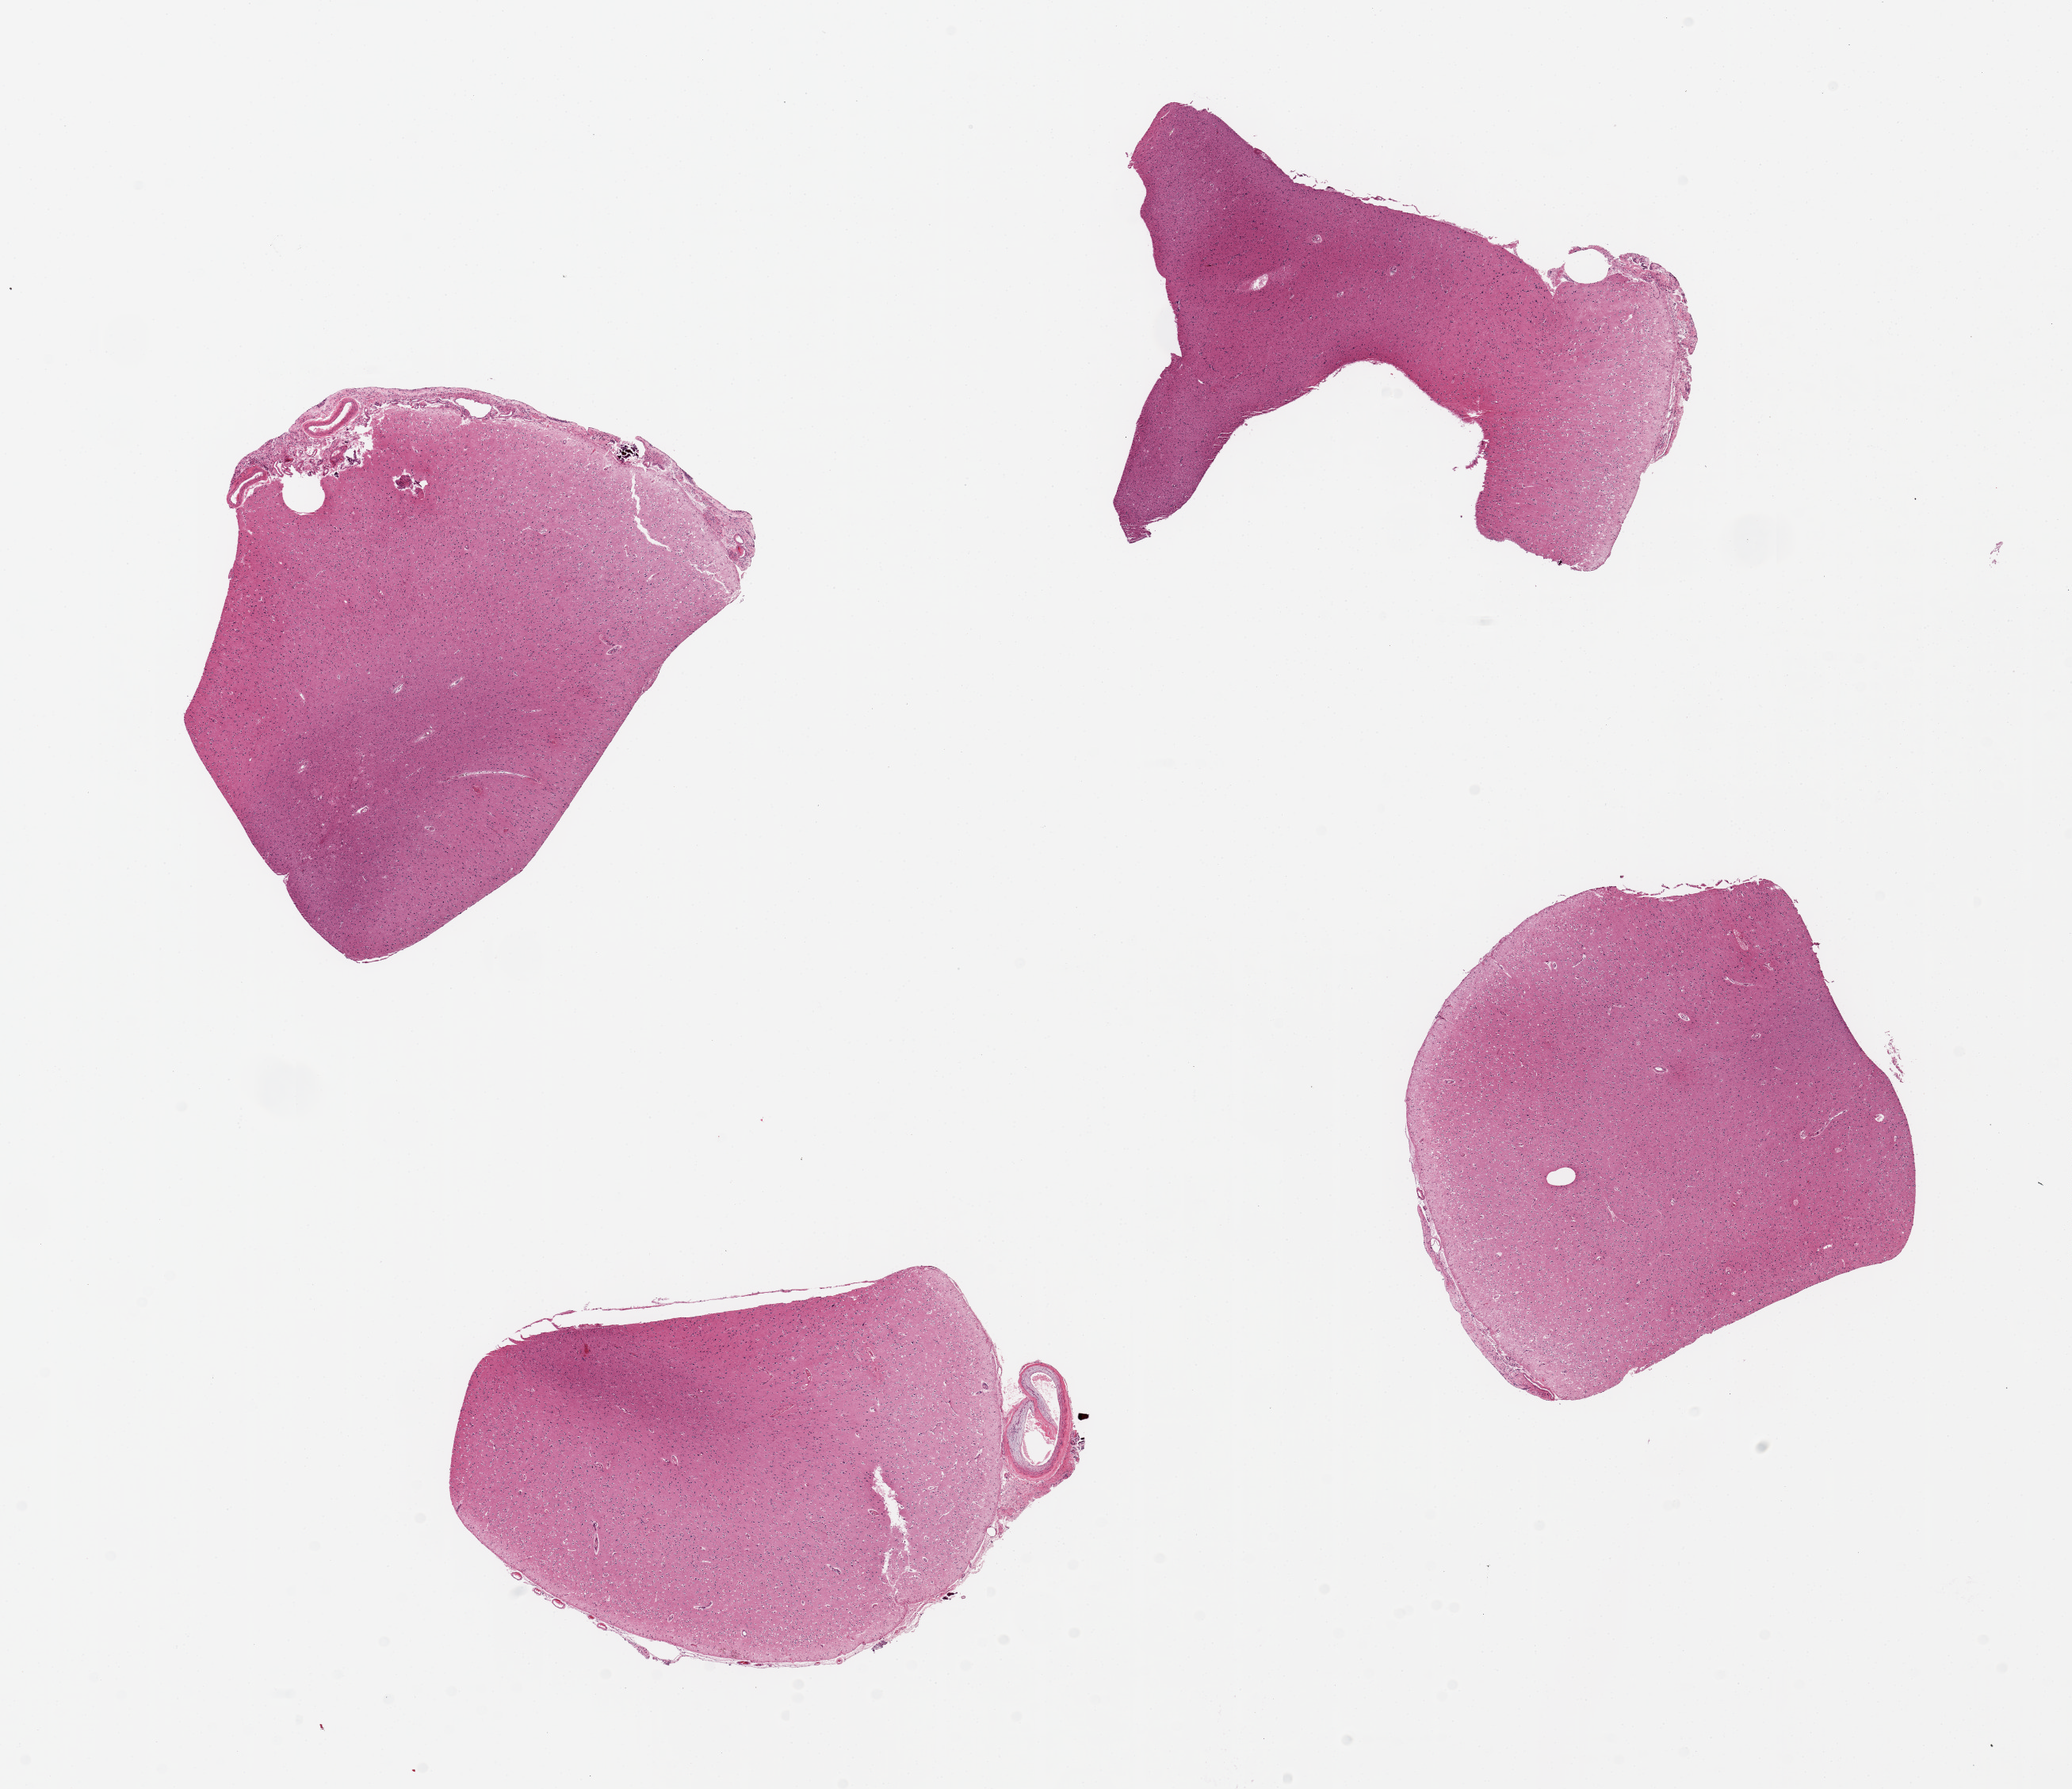
Hematoxylin and eosin (H&E) whole-slide image — low-resolution overview of the scanned area, about 20.7 x 17.8 mm (acquisition: 20x scan). PAXgene-fixed paraffin-embedded (PFPE) section. Section of cerebral cortex (target tissue). Donor tissue sample. Donor: male.
Reviewer comment on this tissue sample: 4 pieces up to 6x5mm.